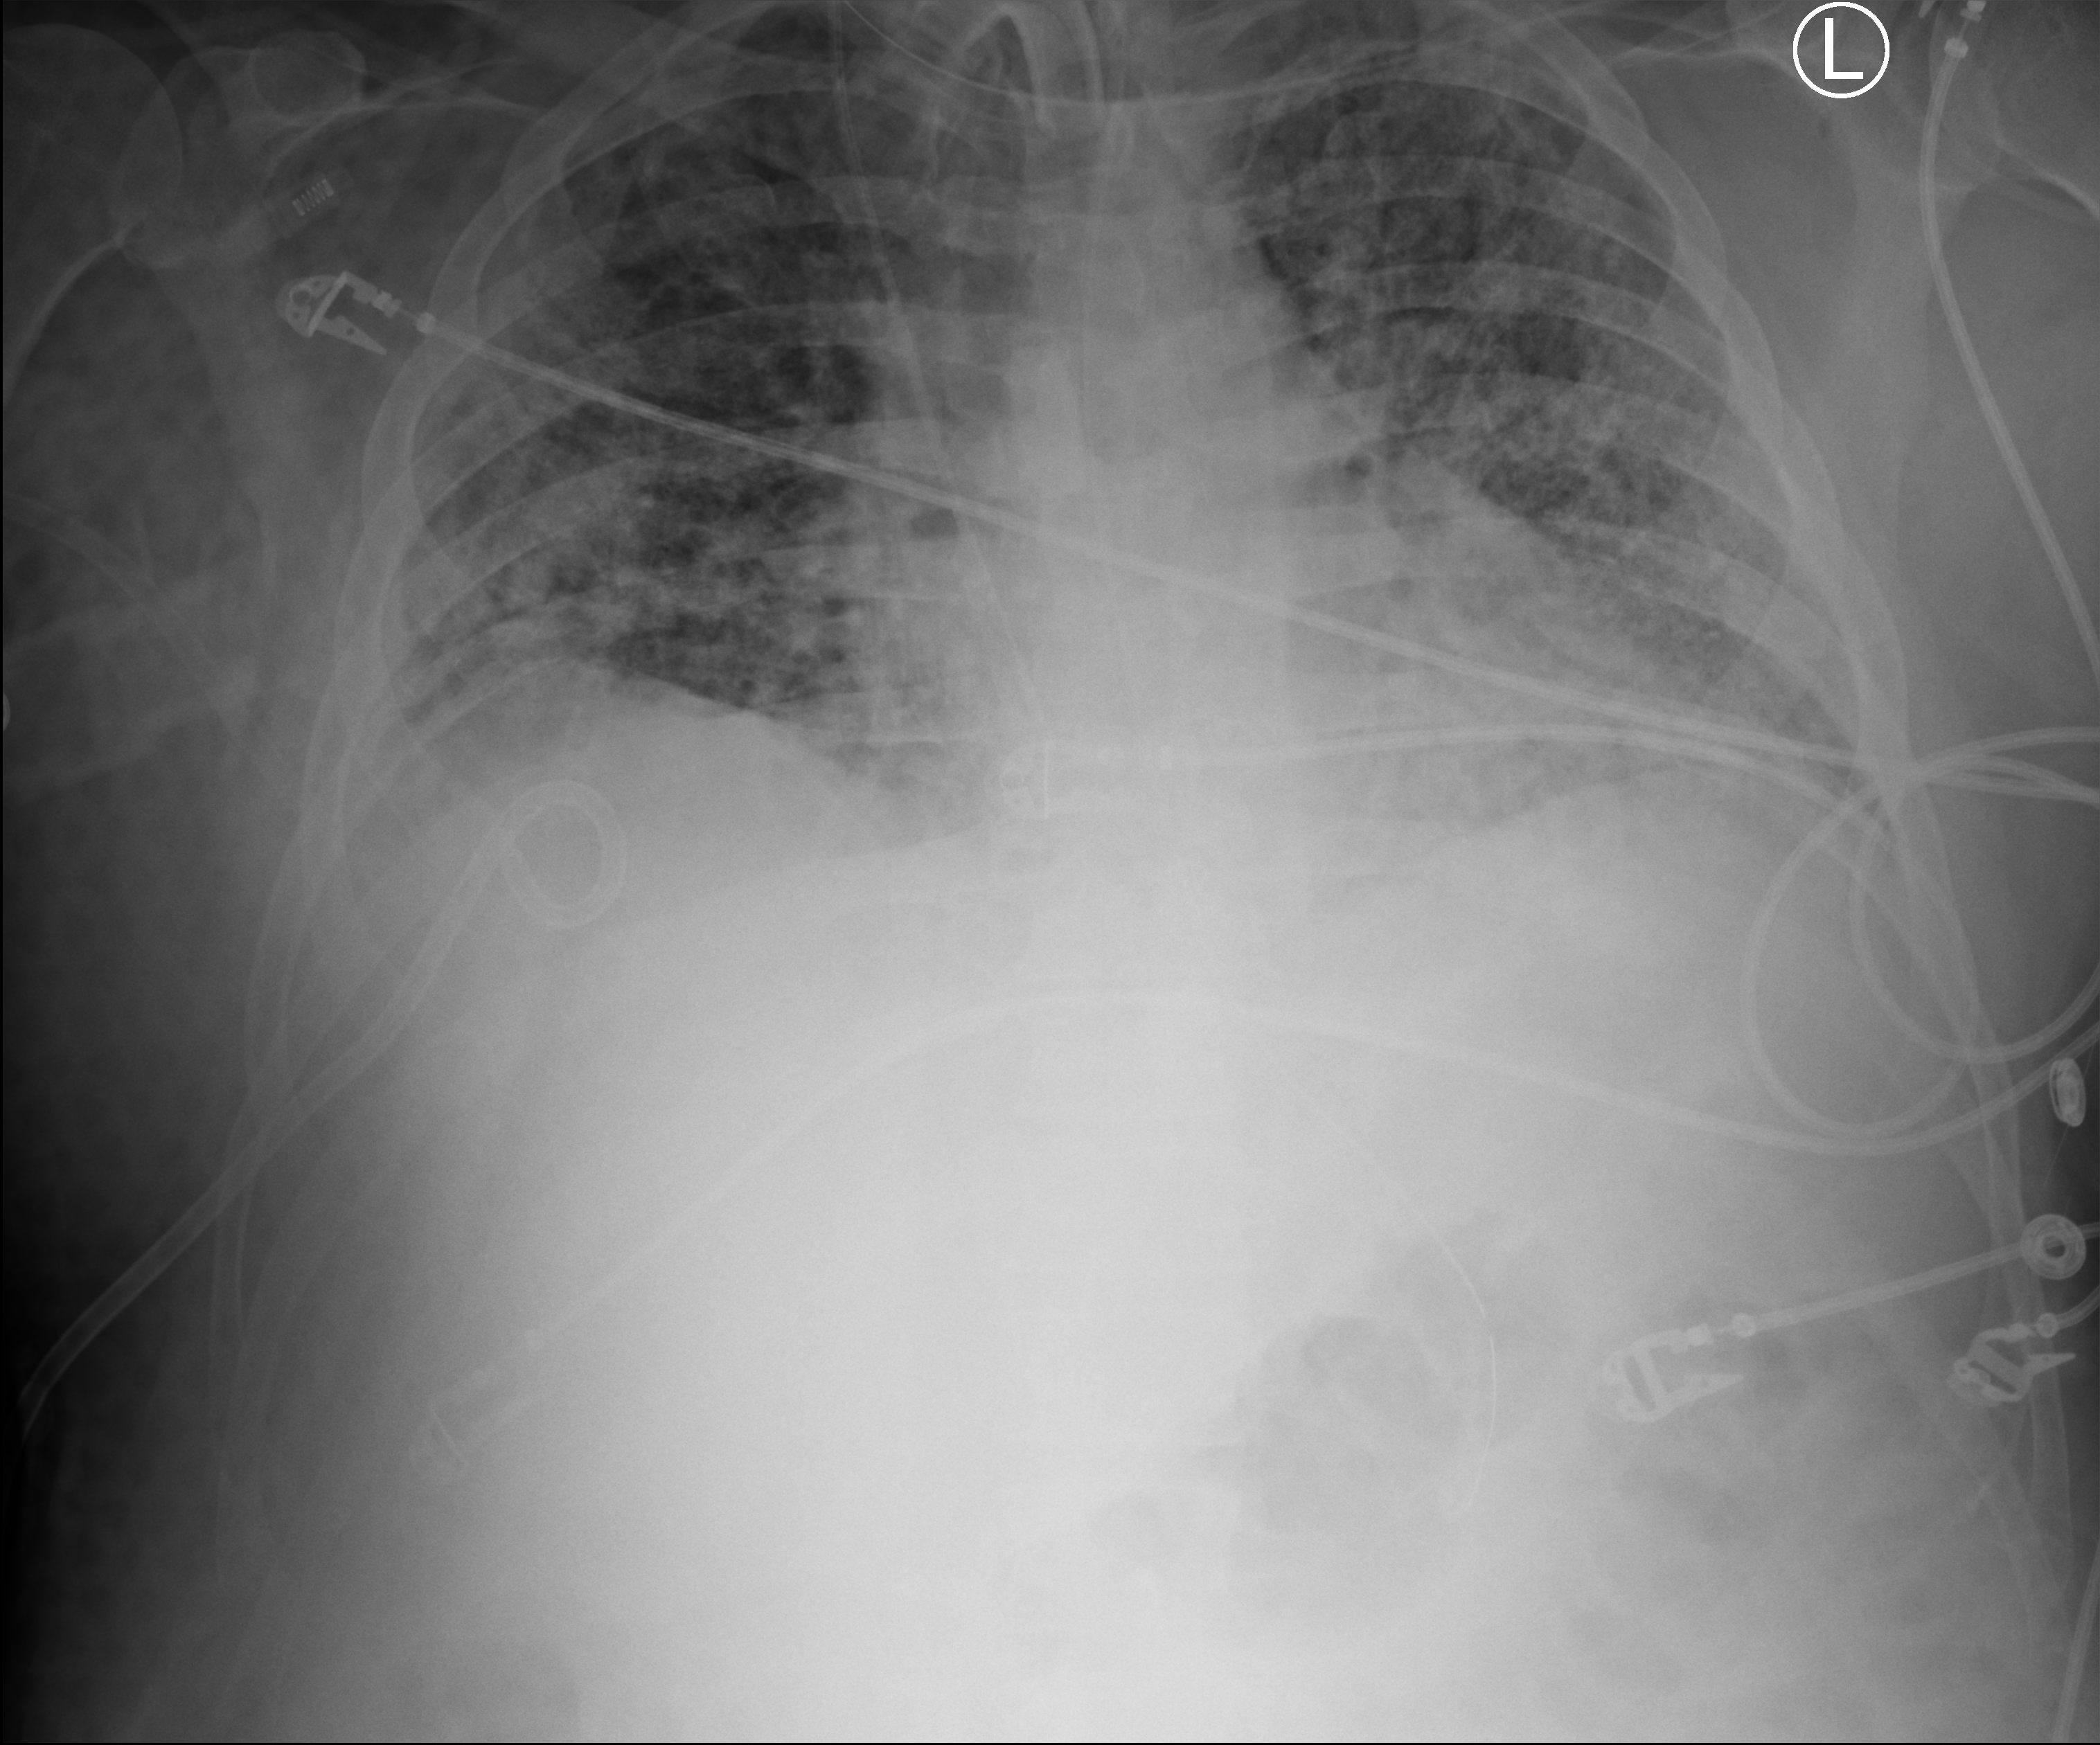
Chest X-ray (portable), anteroposterior (AP) projection. Patient hospitalised with COVID-19; male, aged 18–59 years.
Hospital-stay facts (about this admission, not read from this image; timing relative to this image not recorded): admitted to intensive care during this hospital stay: yes.